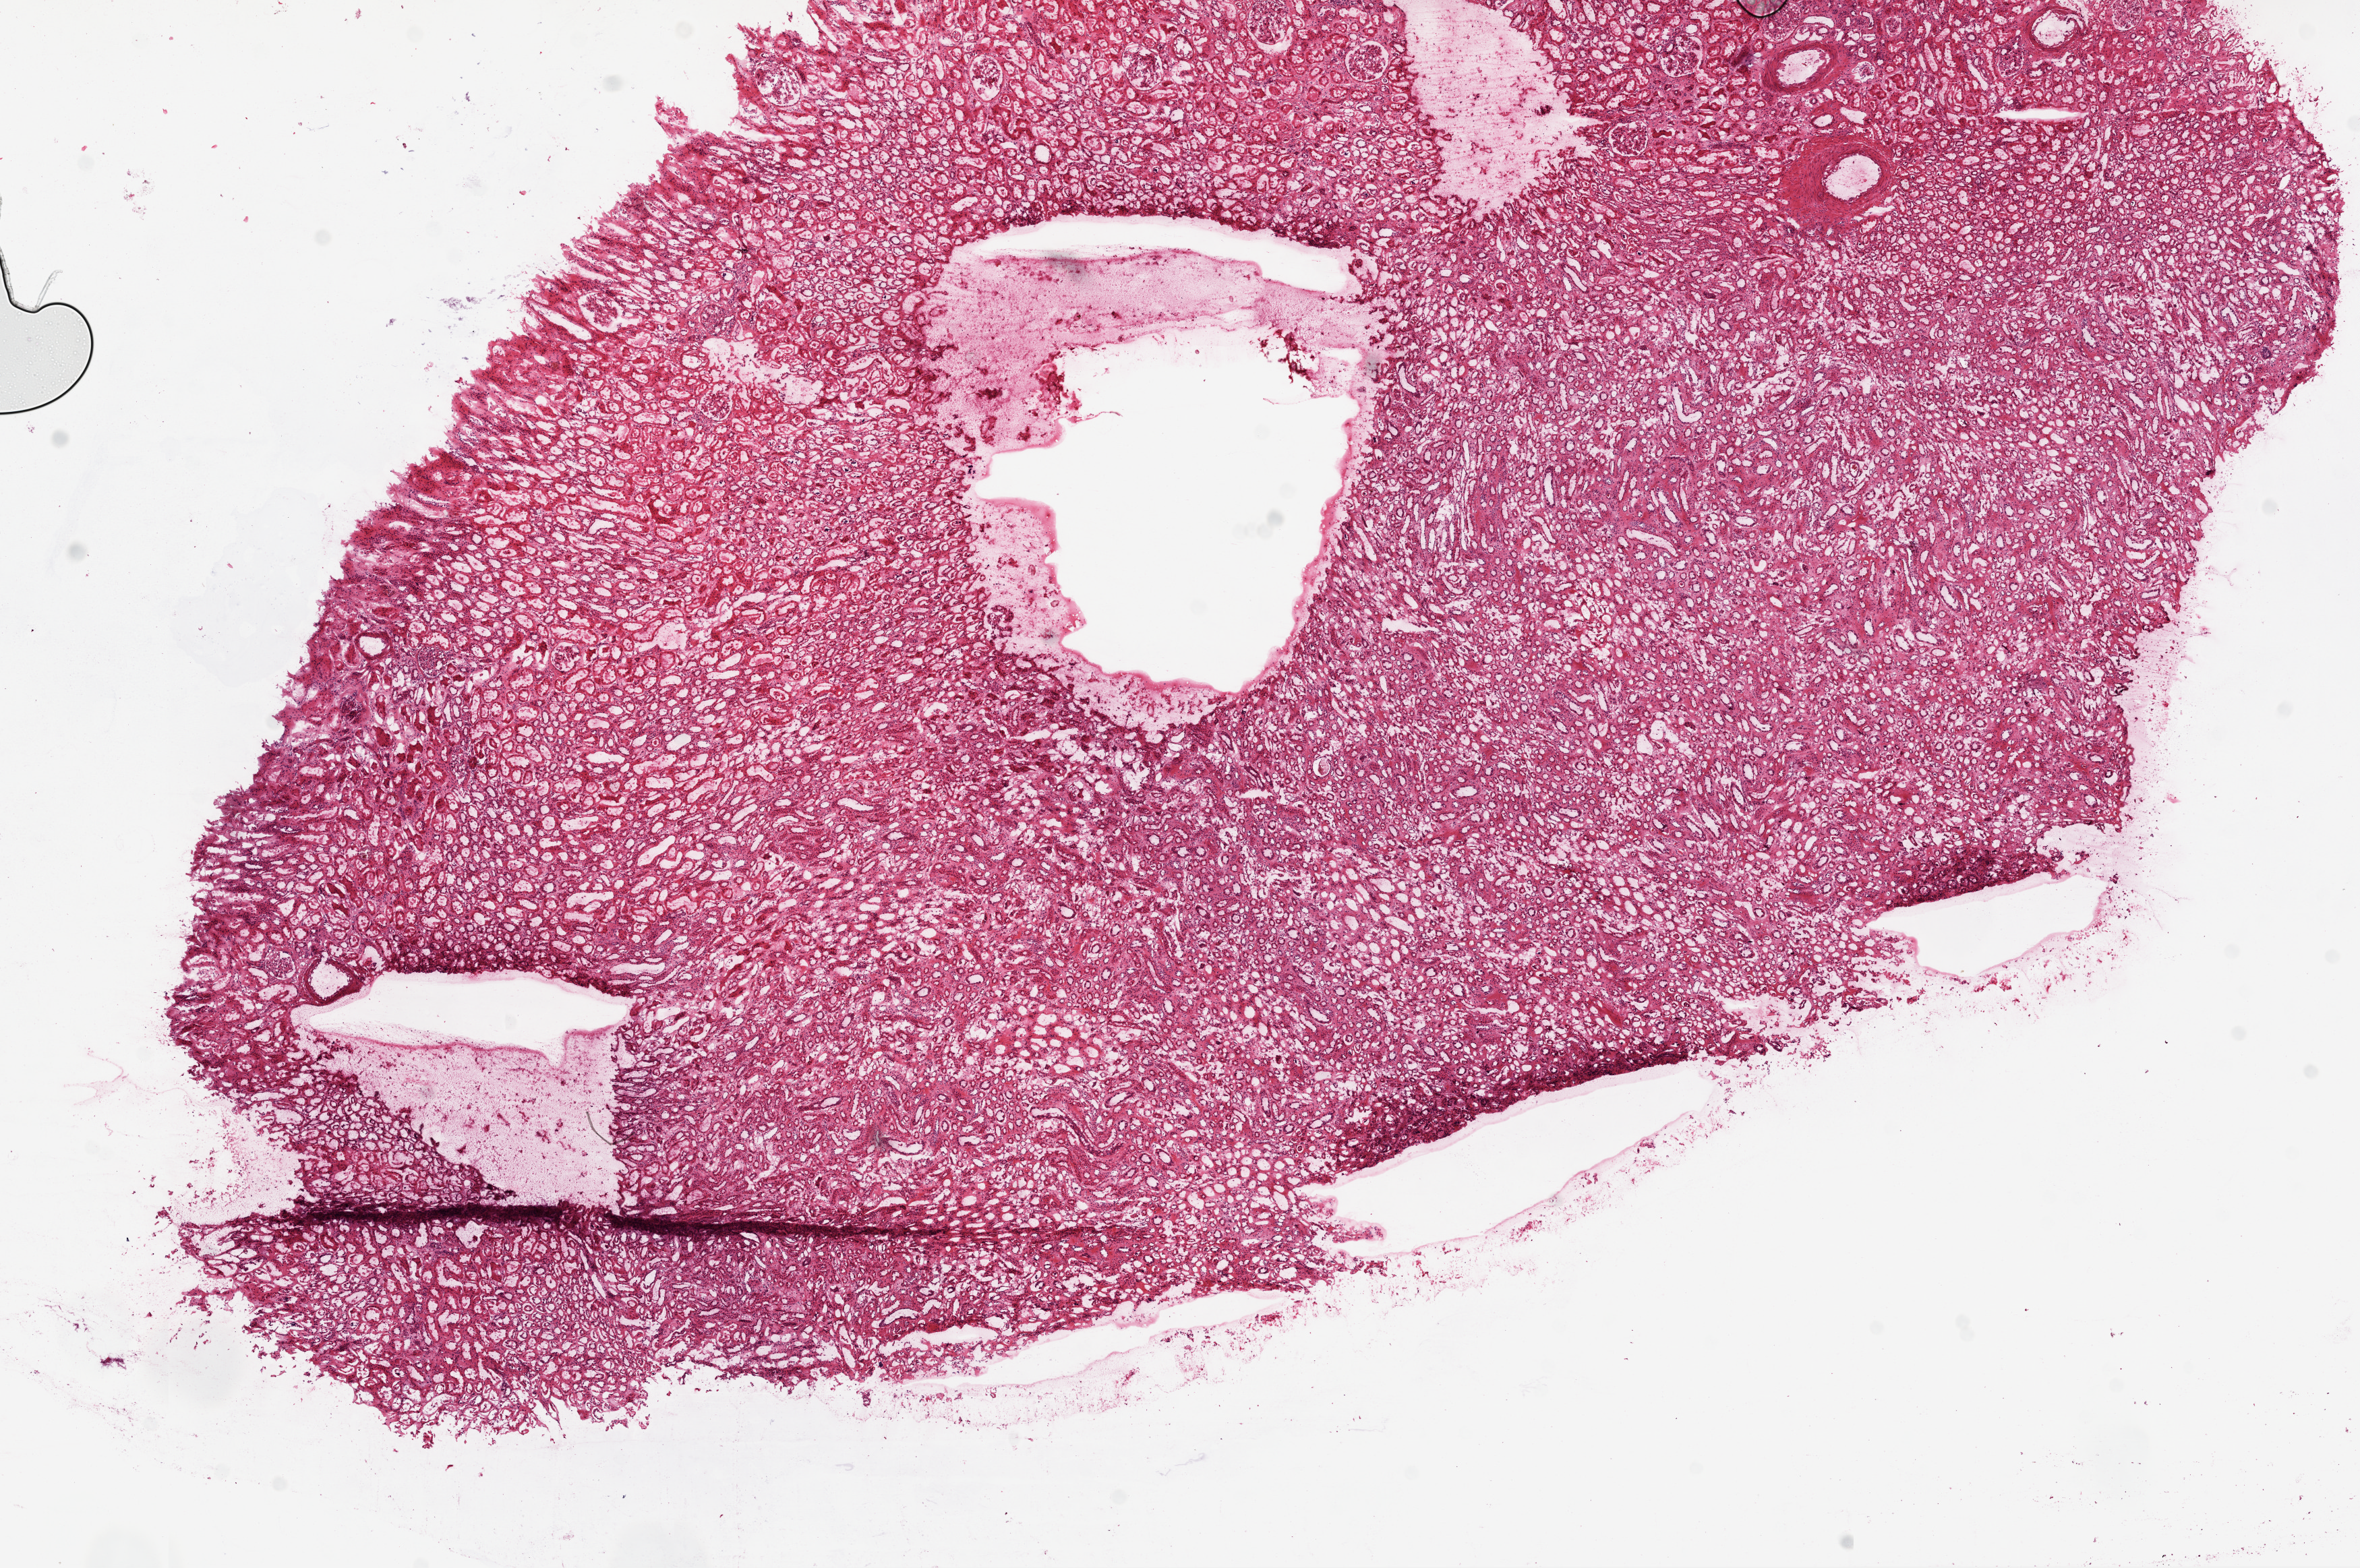
Digitized H&E-stained tissue section (whole slide) — whole scanned area (about 14.0 x 9.3 mm) shown as a low-resolution overview; frozen section from the top of the tissue portion; kidney, solid tissue normal (non-tumour tissue) sample. Male, age 50 years at initial diagnosis.
This section: solid tissue normal (non-tumour) sample from the same patient. Patient diagnosis: Clear cell adenocarcinoma, NOS.